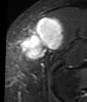
MRI of an extremity soft-tissue mass, one axial slice. Slice 19 of 48 in the series (ordered by position). STIR. MR volume resampled by the dataset authors to the PET/CT grid (not the native acquisition matrix). 87 × 102 image matrix. Female patient. Case-level facts recorded for this patient, not image findings: histological type: synovial sarcoma; grade: intermediate; site of the primary tumour: right thigh.
Annotated regions visible in this slice (expert contour drawn on MRI and transferred to this co-registered scan by the dataset authors):
- gross tumour volume including surrounding oedema: bounding box <17,17,64,60> (left, top, right, bottom; pixels)
- gross tumour volume (mass): <17,17,64,60>